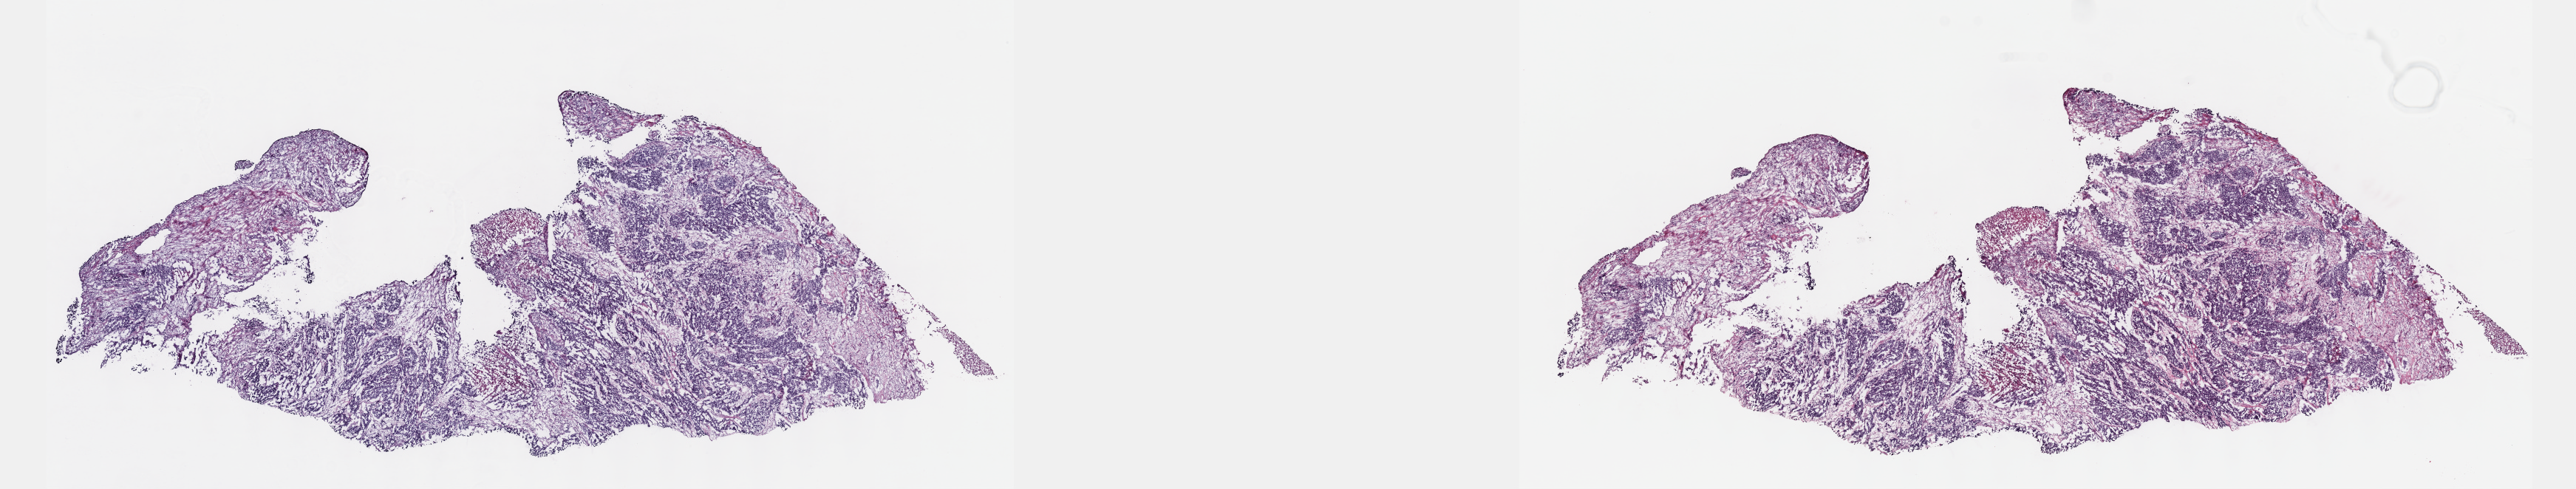
Whole-slide histology image, H&E — whole scanned area (about 28.2 x 5.3 mm) shown as a low-resolution overview. Frozen section. Sample: primary tumour, bladder. Male patient; age at initial diagnosis 49 years.
Diagnosis: Transitional cell carcinoma.